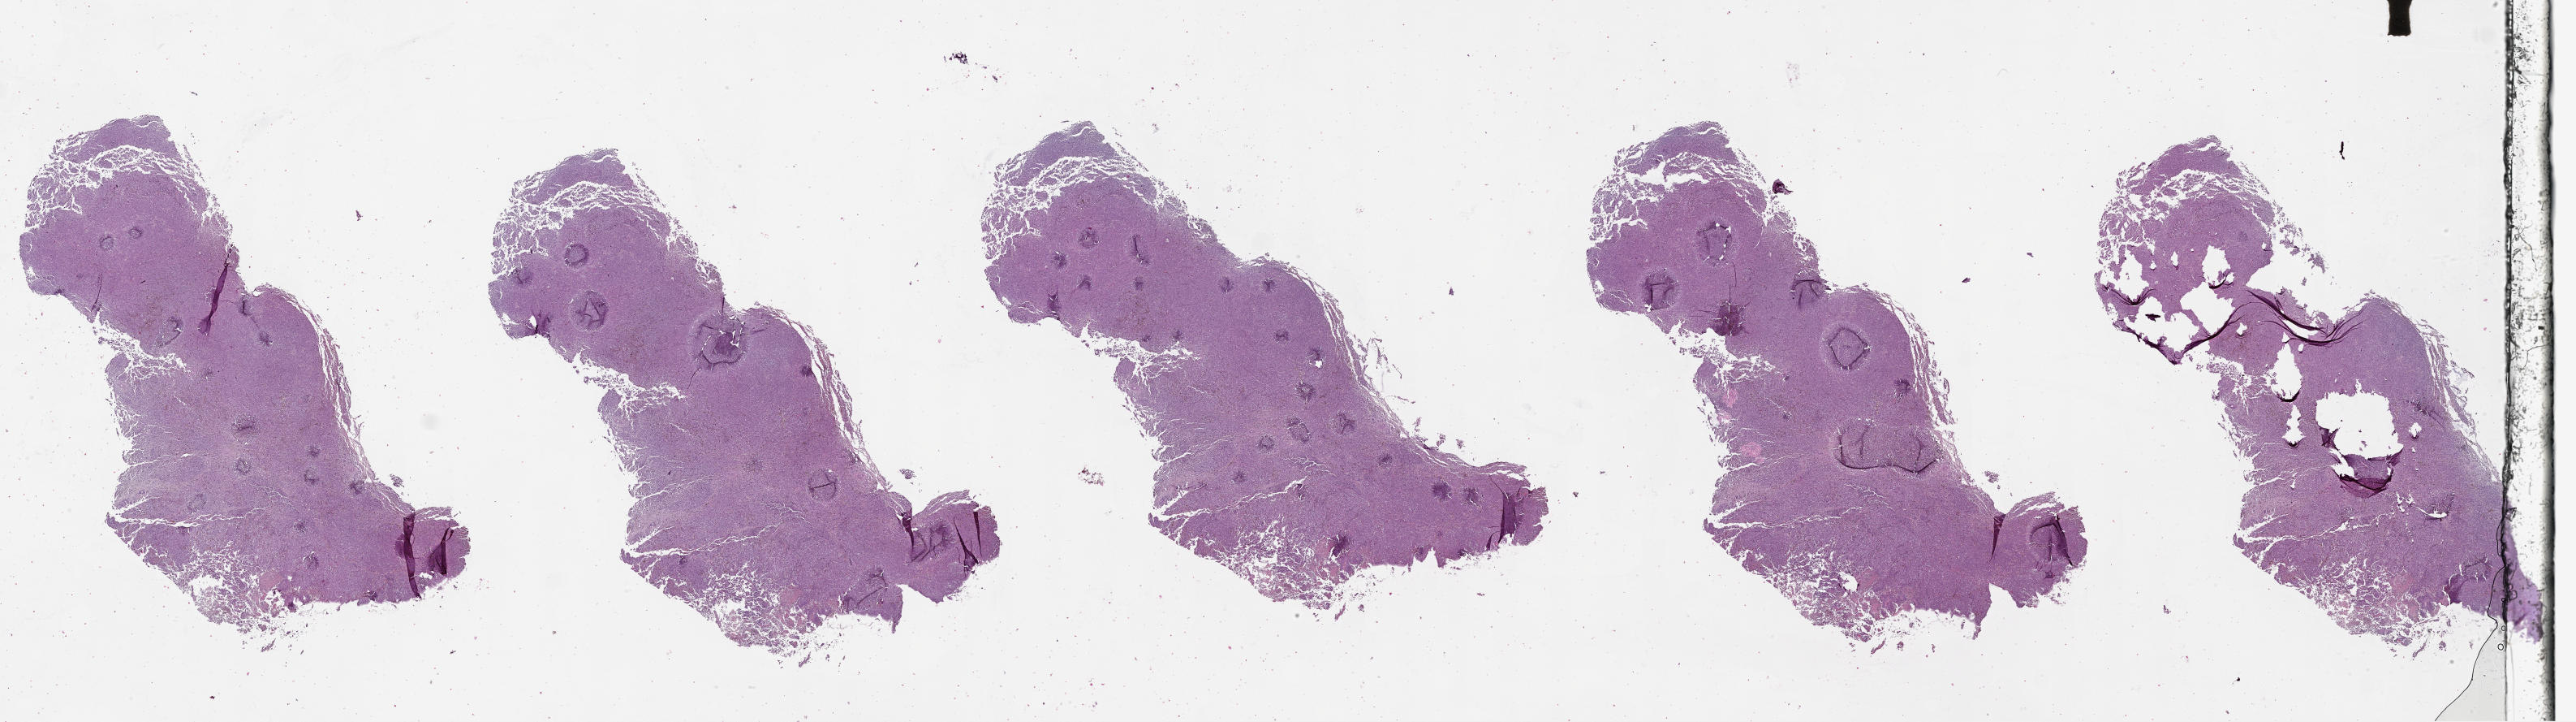
Whole-slide histology image, H&E, a low-resolution overview of the entire scanned area, about 51.1 x 14.3 mm (acquisition: 20x scan). Female, 70 y/o.
Patient diagnosis: Malignant melanoma, NOS.